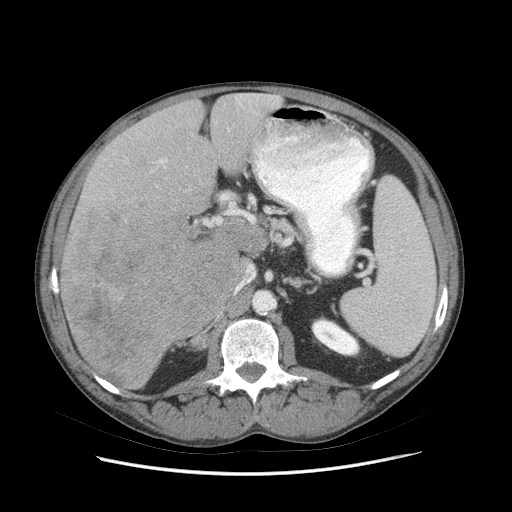
Contrast-enhanced abdominal CT (liver protocol), one axial slice. Position 41 of 89 along the scan axis. Reconstruction kernel STANDARD. 140 kVp. Soft-tissue window (W 400 / L 40 HU). 2.5 mm slice thickness. 512 × 512 image matrix, field of view 380 × 380 mm. From the clinical record (not read from this slice): diagnosis: hepatocellular carcinoma (patient treated with transarterial chemoembolisation; whether this scan precedes or follows treatment is not stated here); TNM stage (as recorded): Stage-IIIB; Child-Pugh class: A; tumour differentiation: moderately differentiated; tumour nodularity: multinodular.
Outlined on this slice (semi-automatically segmented with operator editing):
- liver parenchyma outside the tumour (the mass and vessels are separate outlines, so this box may not span the whole liver): bounding box (x1, y1, x2, y2) in pixels: (58, 92, 282, 390)
- mass: (59, 207, 237, 387)
- liver vessels: (159, 94, 278, 224)